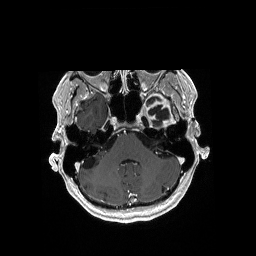
Brain MRI from a brain-tumour surgery series, one axial slice. Position 134 of 176 along the scan axis. T1-weighted post-contrast. 1 mm slice thickness. 256 × 256 image matrix, field of view 256 × 256 mm. From the clinical record (not read from this slice): histopathology: Glioblastoma; WHO grade: 4; IDH mutation: no.
Structures marked on this image (outlined manually by an expert reader):
- previous resection cavity: bounding box (x1, y1, x2, y2) in pixels: (148, 105, 169, 122)